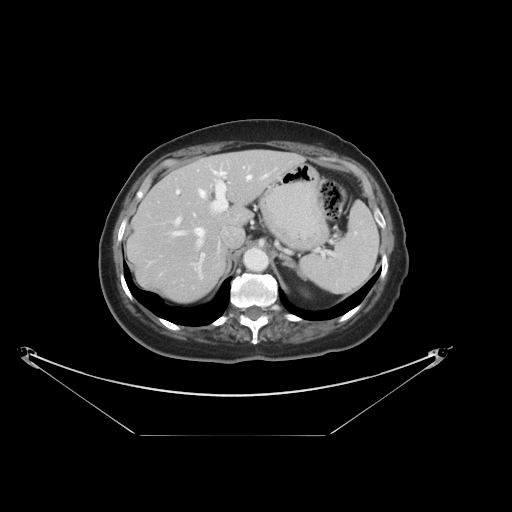
Contrast-enhanced abdominal CT, one axial slice. Slice 25 of 36 in the series (ordered by position). Reconstruction kernel STANDARD. 120 kVp. Intravenous contrast given. Soft-tissue window (W 400 / L 40 HU). 512 × 512 image matrix, field of view 500 × 500 mm. Female patient, age 70 years. From the clinical record (not read from this slice): diagnosis: colorectal cancer liver metastases, imaged before liver resection; multiple liver metastases: no; largest metastasis: 2.5 cm; disease in both lobes: no.
Outlined on this slice (expert manual segmentation):
- hepatic veins: bounding box <166,171,267,238> (left, top, right, bottom; pixels)
- liver: <127,151,302,302>
- planned liver remnant (the part of the liver to remain after resection): <127,151,302,302>
- portal vein (with intrahepatic branches): <174,169,228,279>